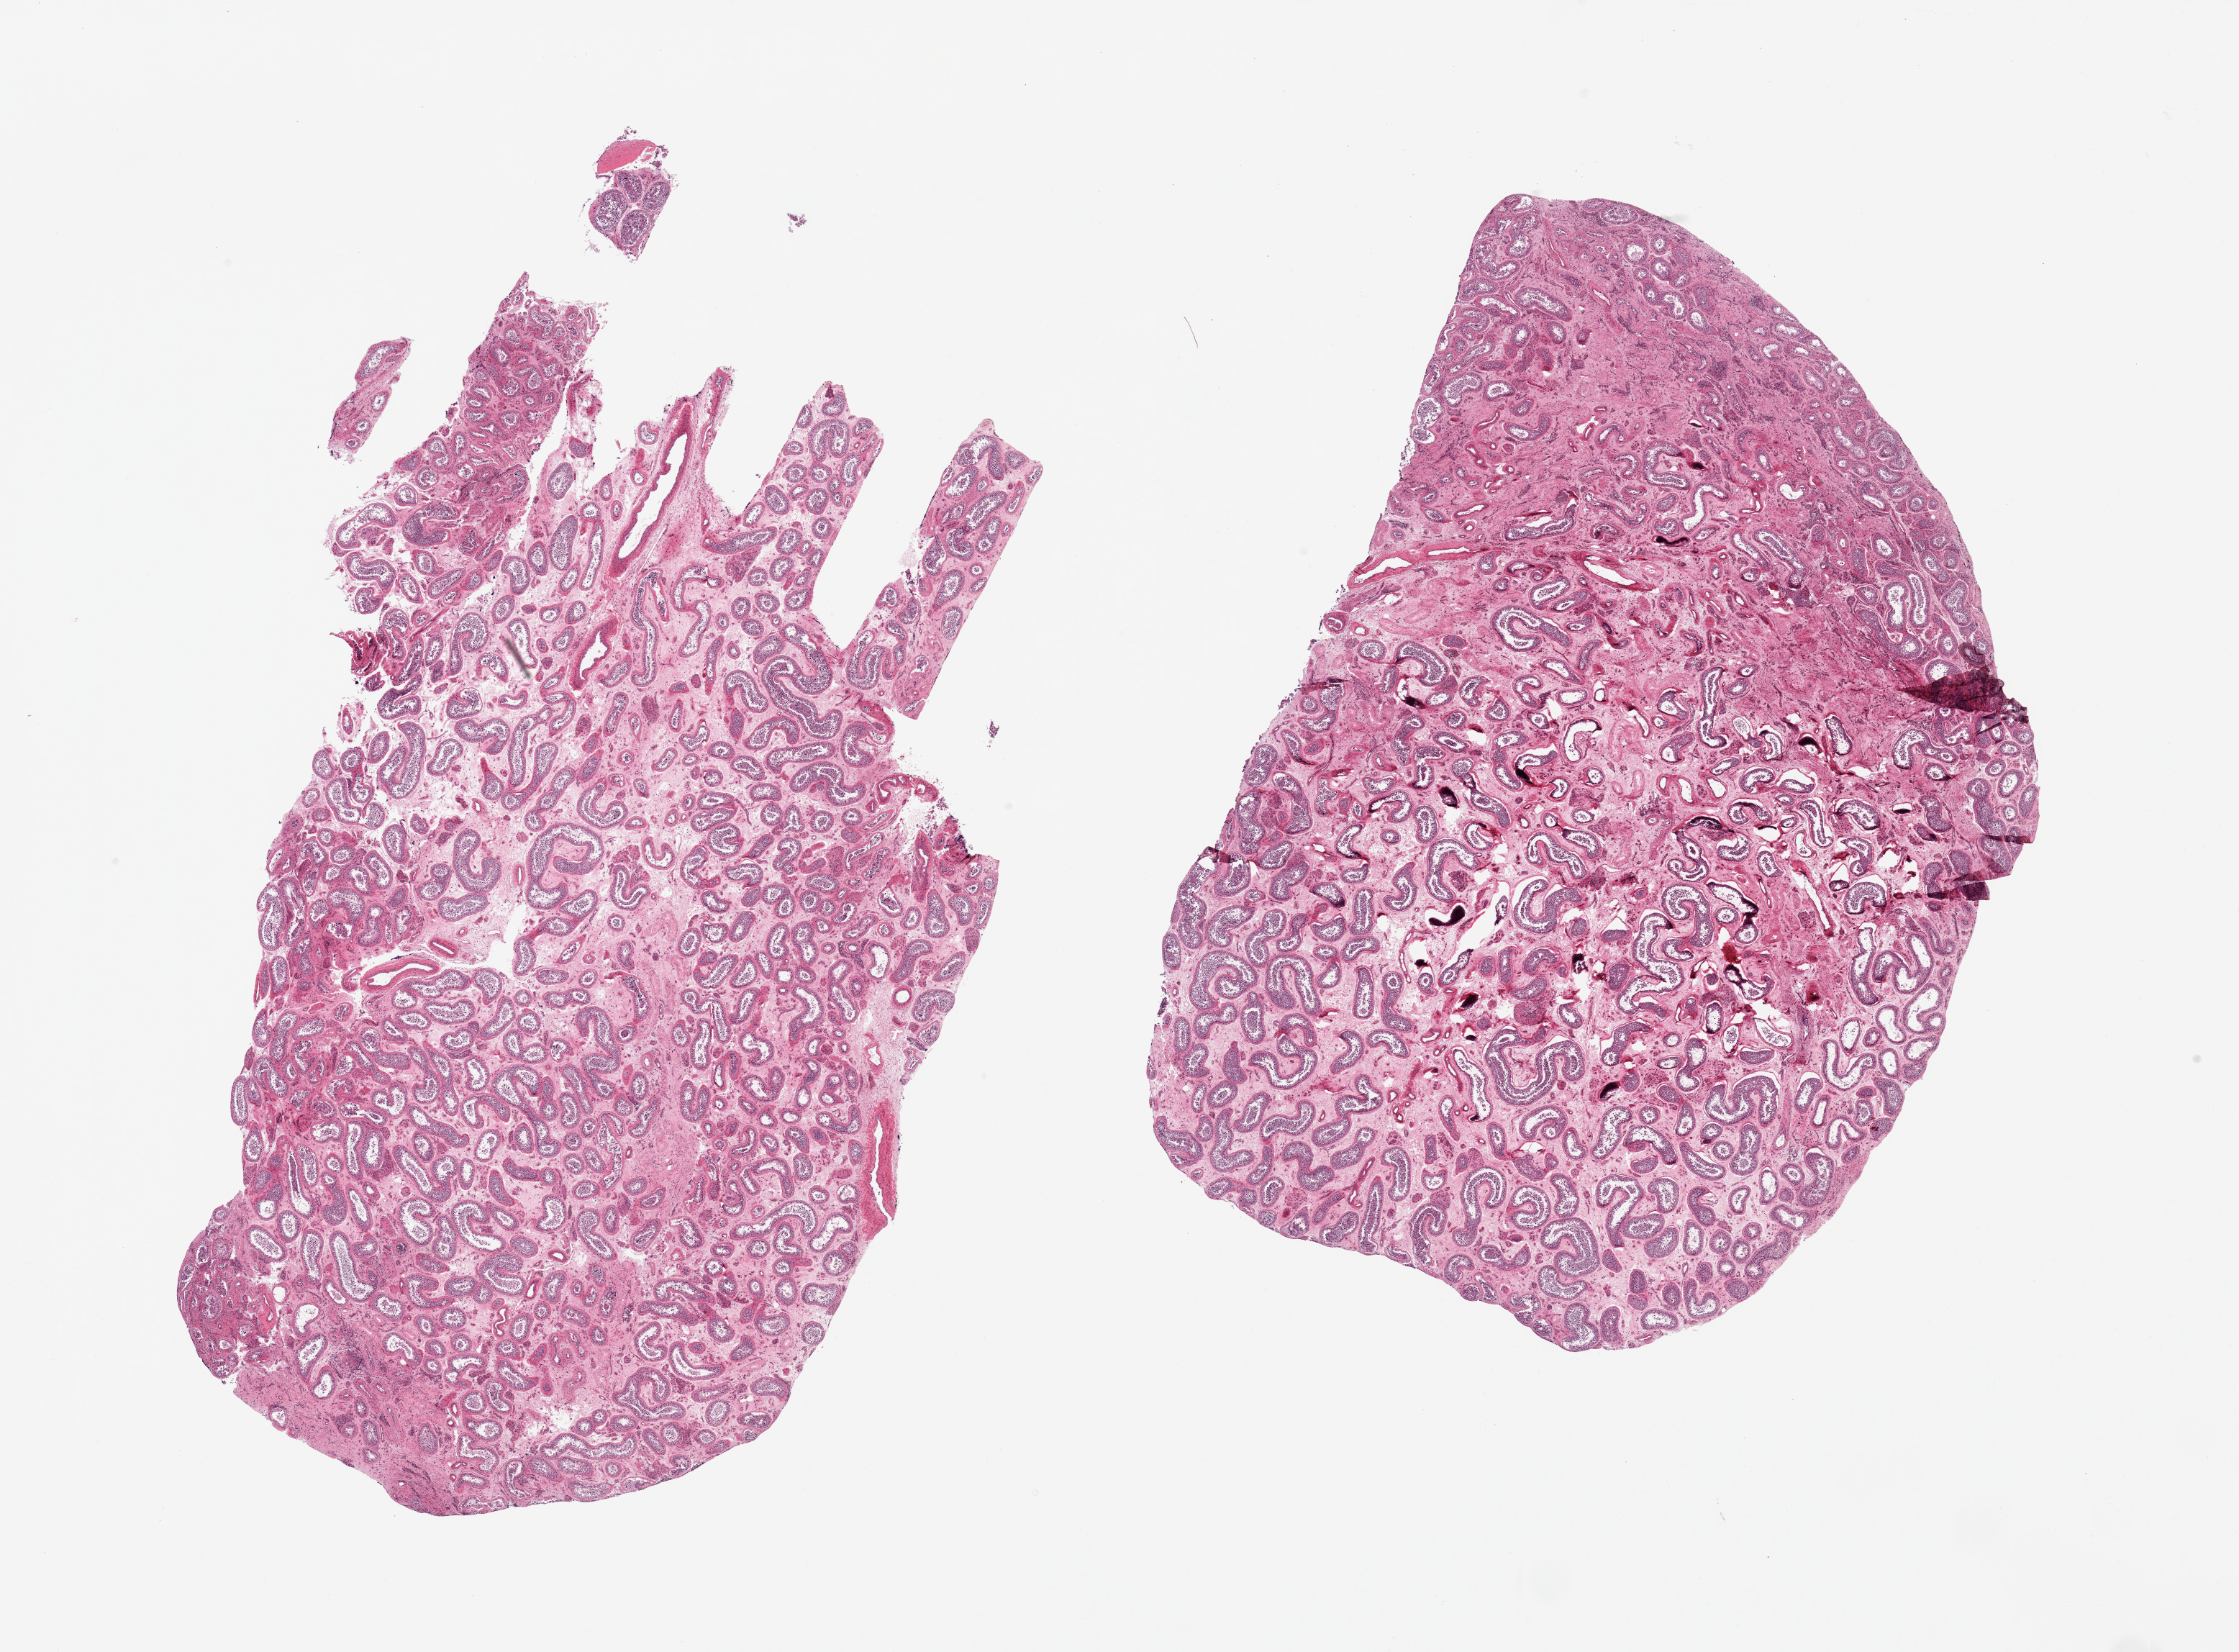
Hematoxylin and eosin (H&E) whole-slide image, shown as a low-resolution overview of the whole scanned area (about 24.6 x 18.2 mm). PAXgene-fixed paraffin-embedded (PFPE) section. Sampled site (target tissue): testis. Tissue donor sample. Donor sex: male.
- pathologist's review note for this sample: 2 pieces; spermatogenesis is present, some hyalinized tubules